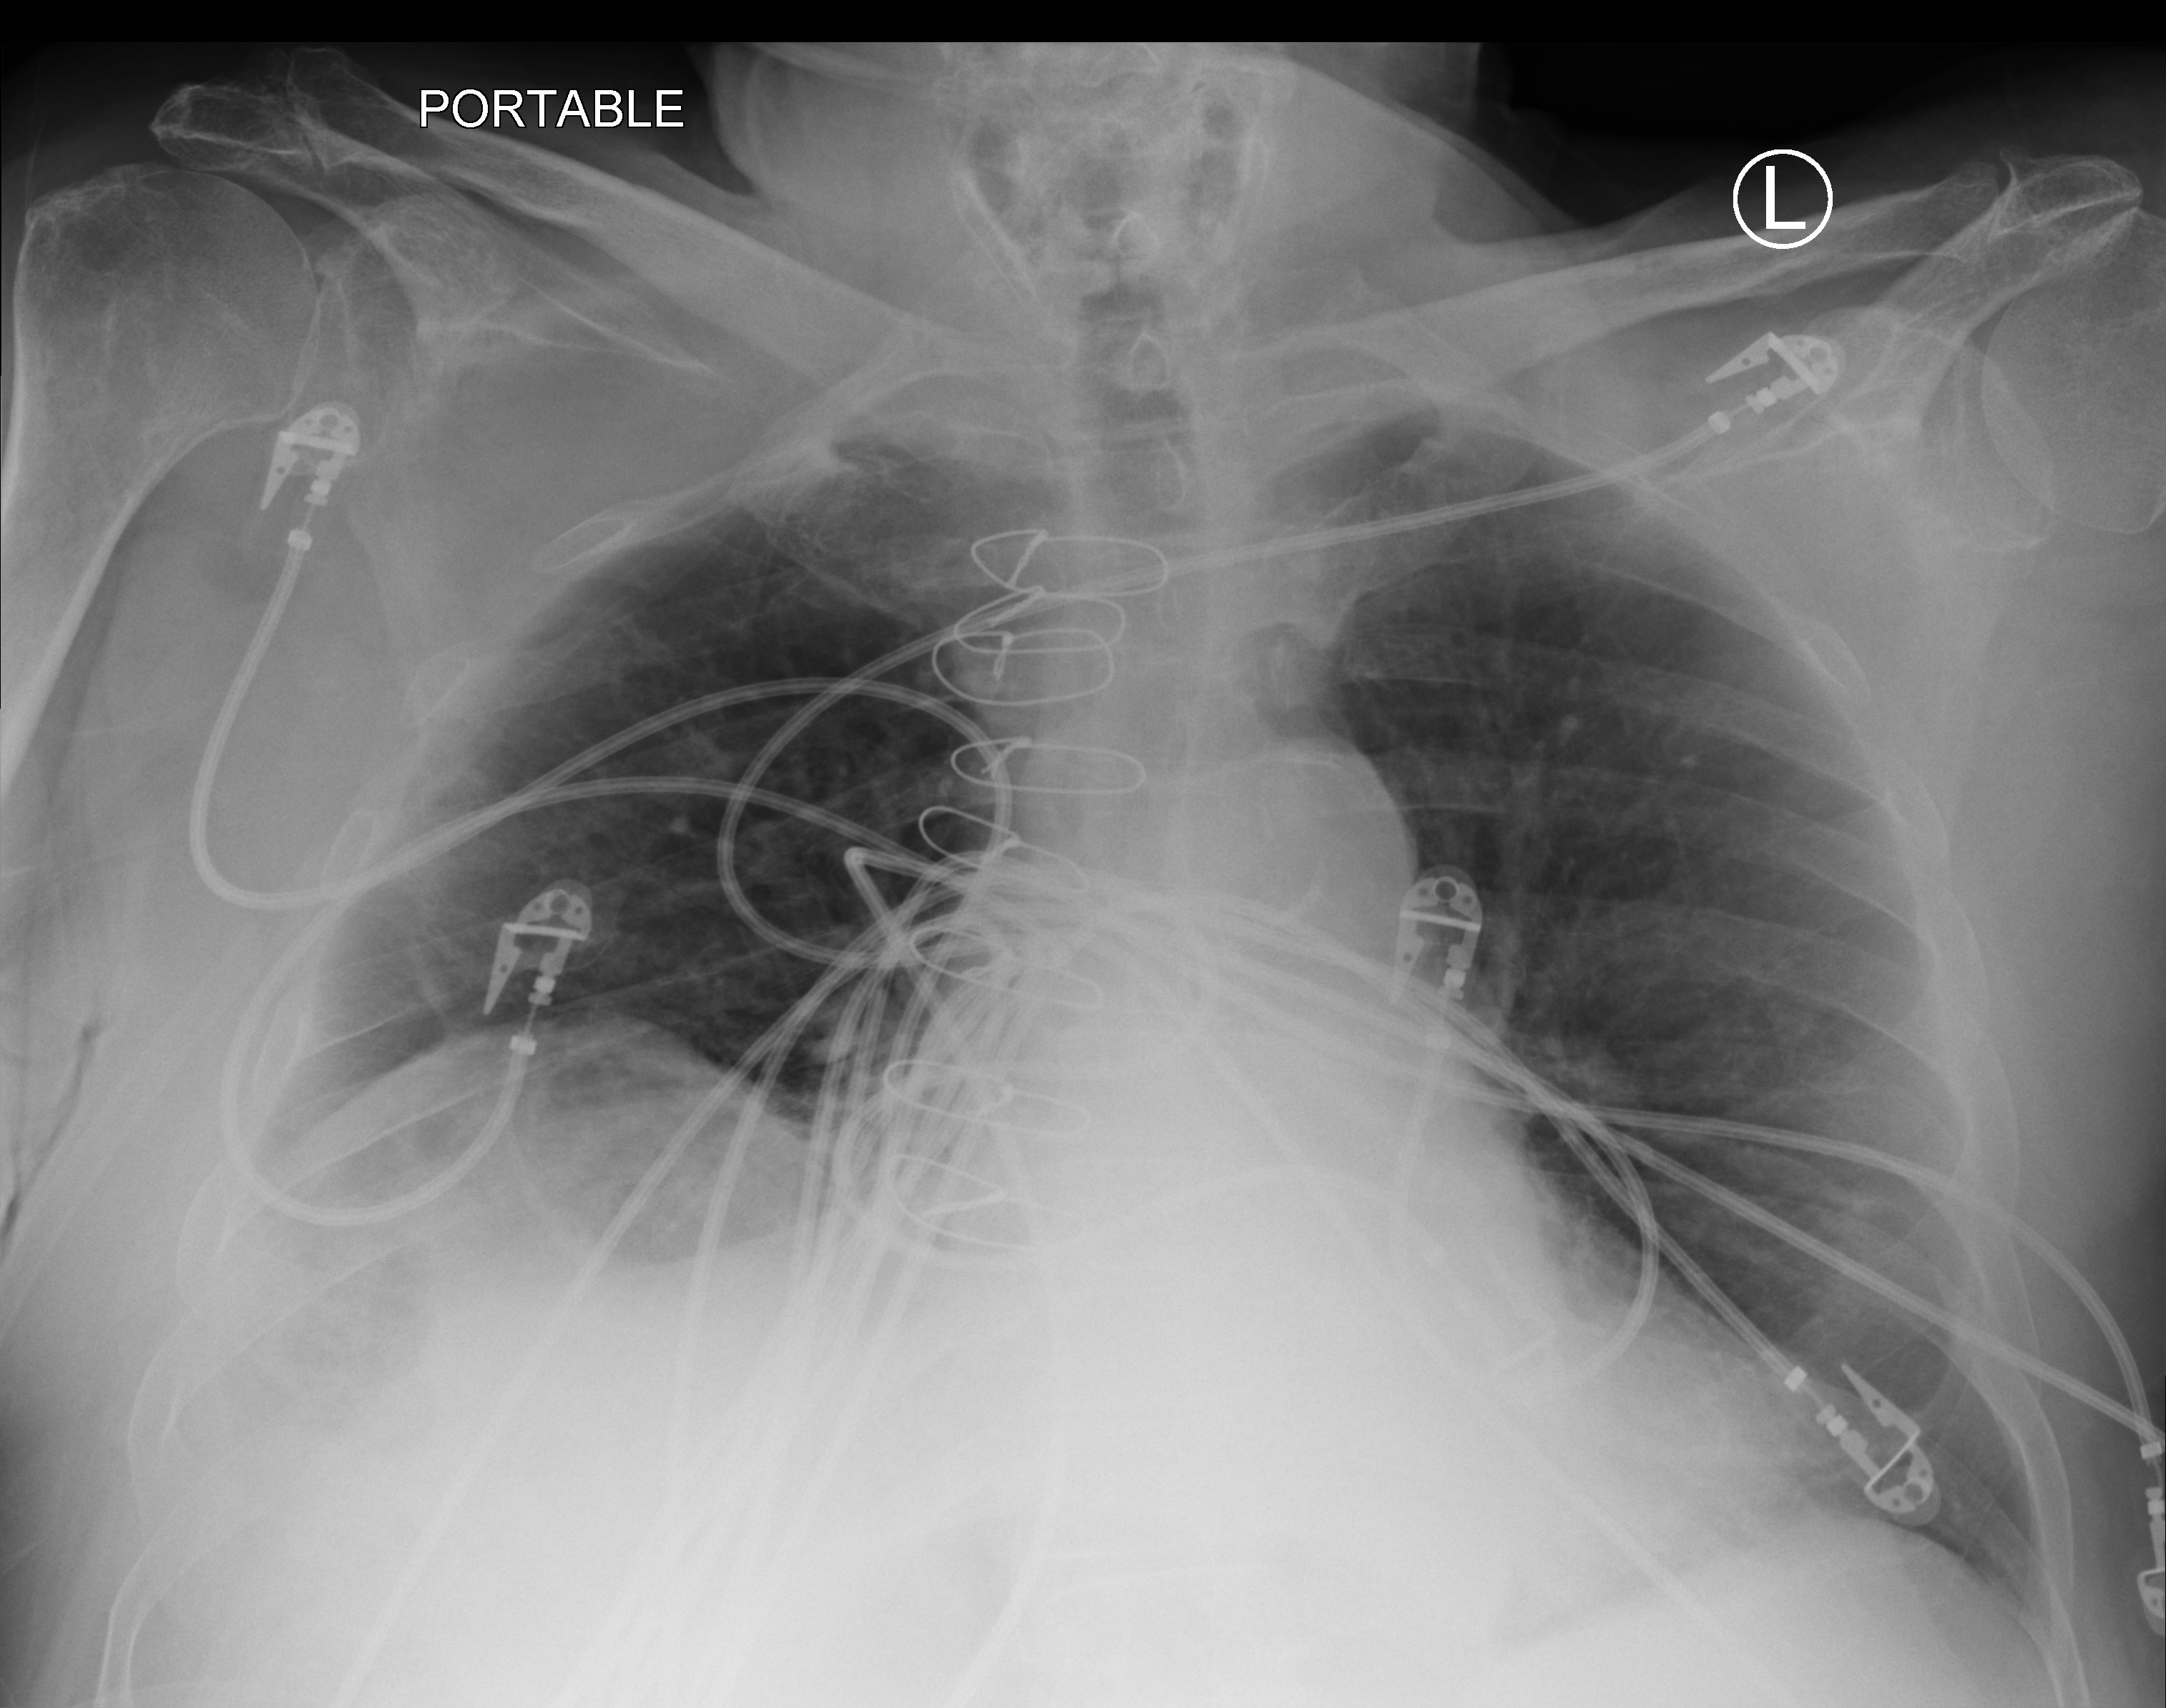
Bedside chest radiograph (computed radiography), anteroposterior (AP) projection. Patient hospitalised with COVID-19; male, aged 75–90 years.
Admission-level facts for this patient (not findings on this image; timing relative to this image not recorded):
- mechanically ventilated during this hospital stay: no